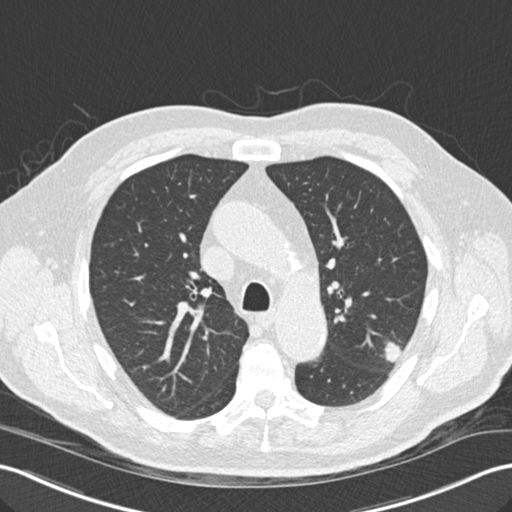
Low-dose screening chest CT, one axial slice. Position 104 of 157 along the scan axis. 120 kVp. Lung window (W 1500 / L -600 HU). 2 mm slice thickness. 512 × 512 image matrix, field of view 354 × 354 mm.
Outlined on this slice (expert manual segmentation):
- lesion 1 (tumor, upper lobe of left lung): bounding box [x1, y1, x2, y2] px = [385, 342, 401, 362]